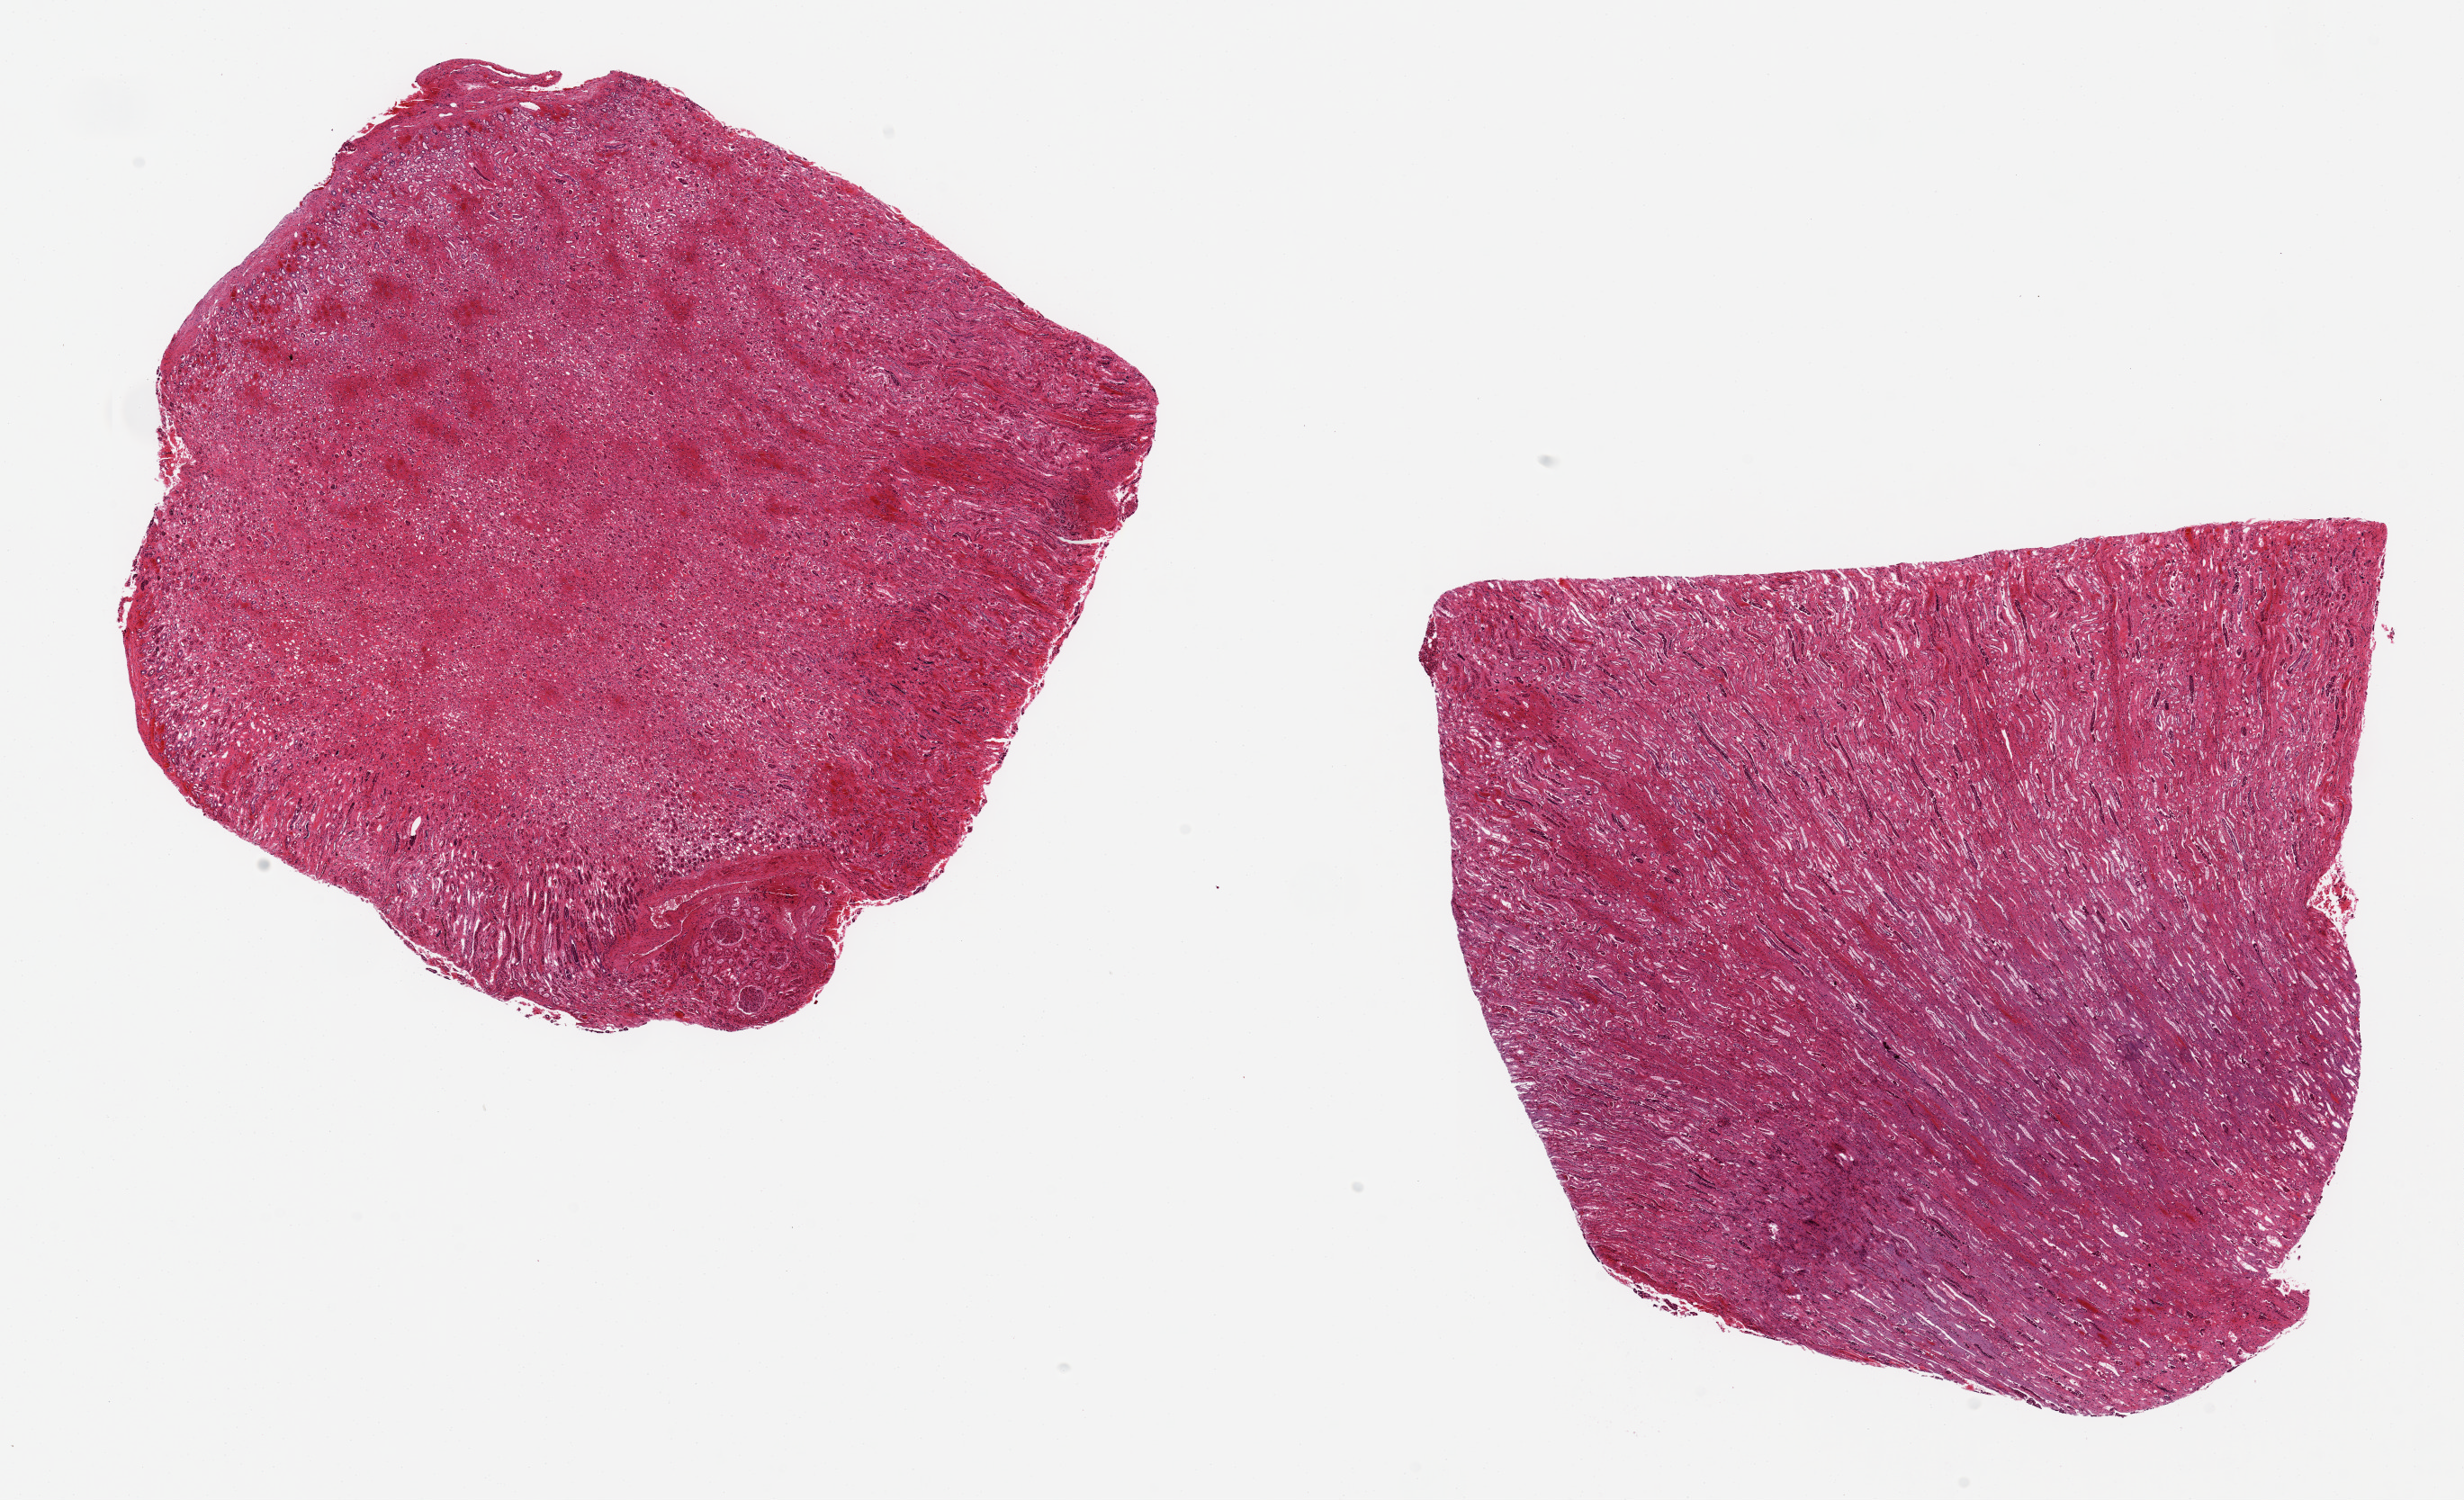
Whole-slide image, hematoxylin and eosin (H&E) stain — low-resolution overview of the scanned area, about 21.7 x 13.2 mm. PAXgene-fixed paraffin-embedded (PFPE) section. Sampled site (target tissue): renal medulla. Donor tissue sample. Male donor.
Reviewer comment on this tissue sample: 2 pieces 8x7 & 7x6 mm; <5% focus of cortex at one edge.